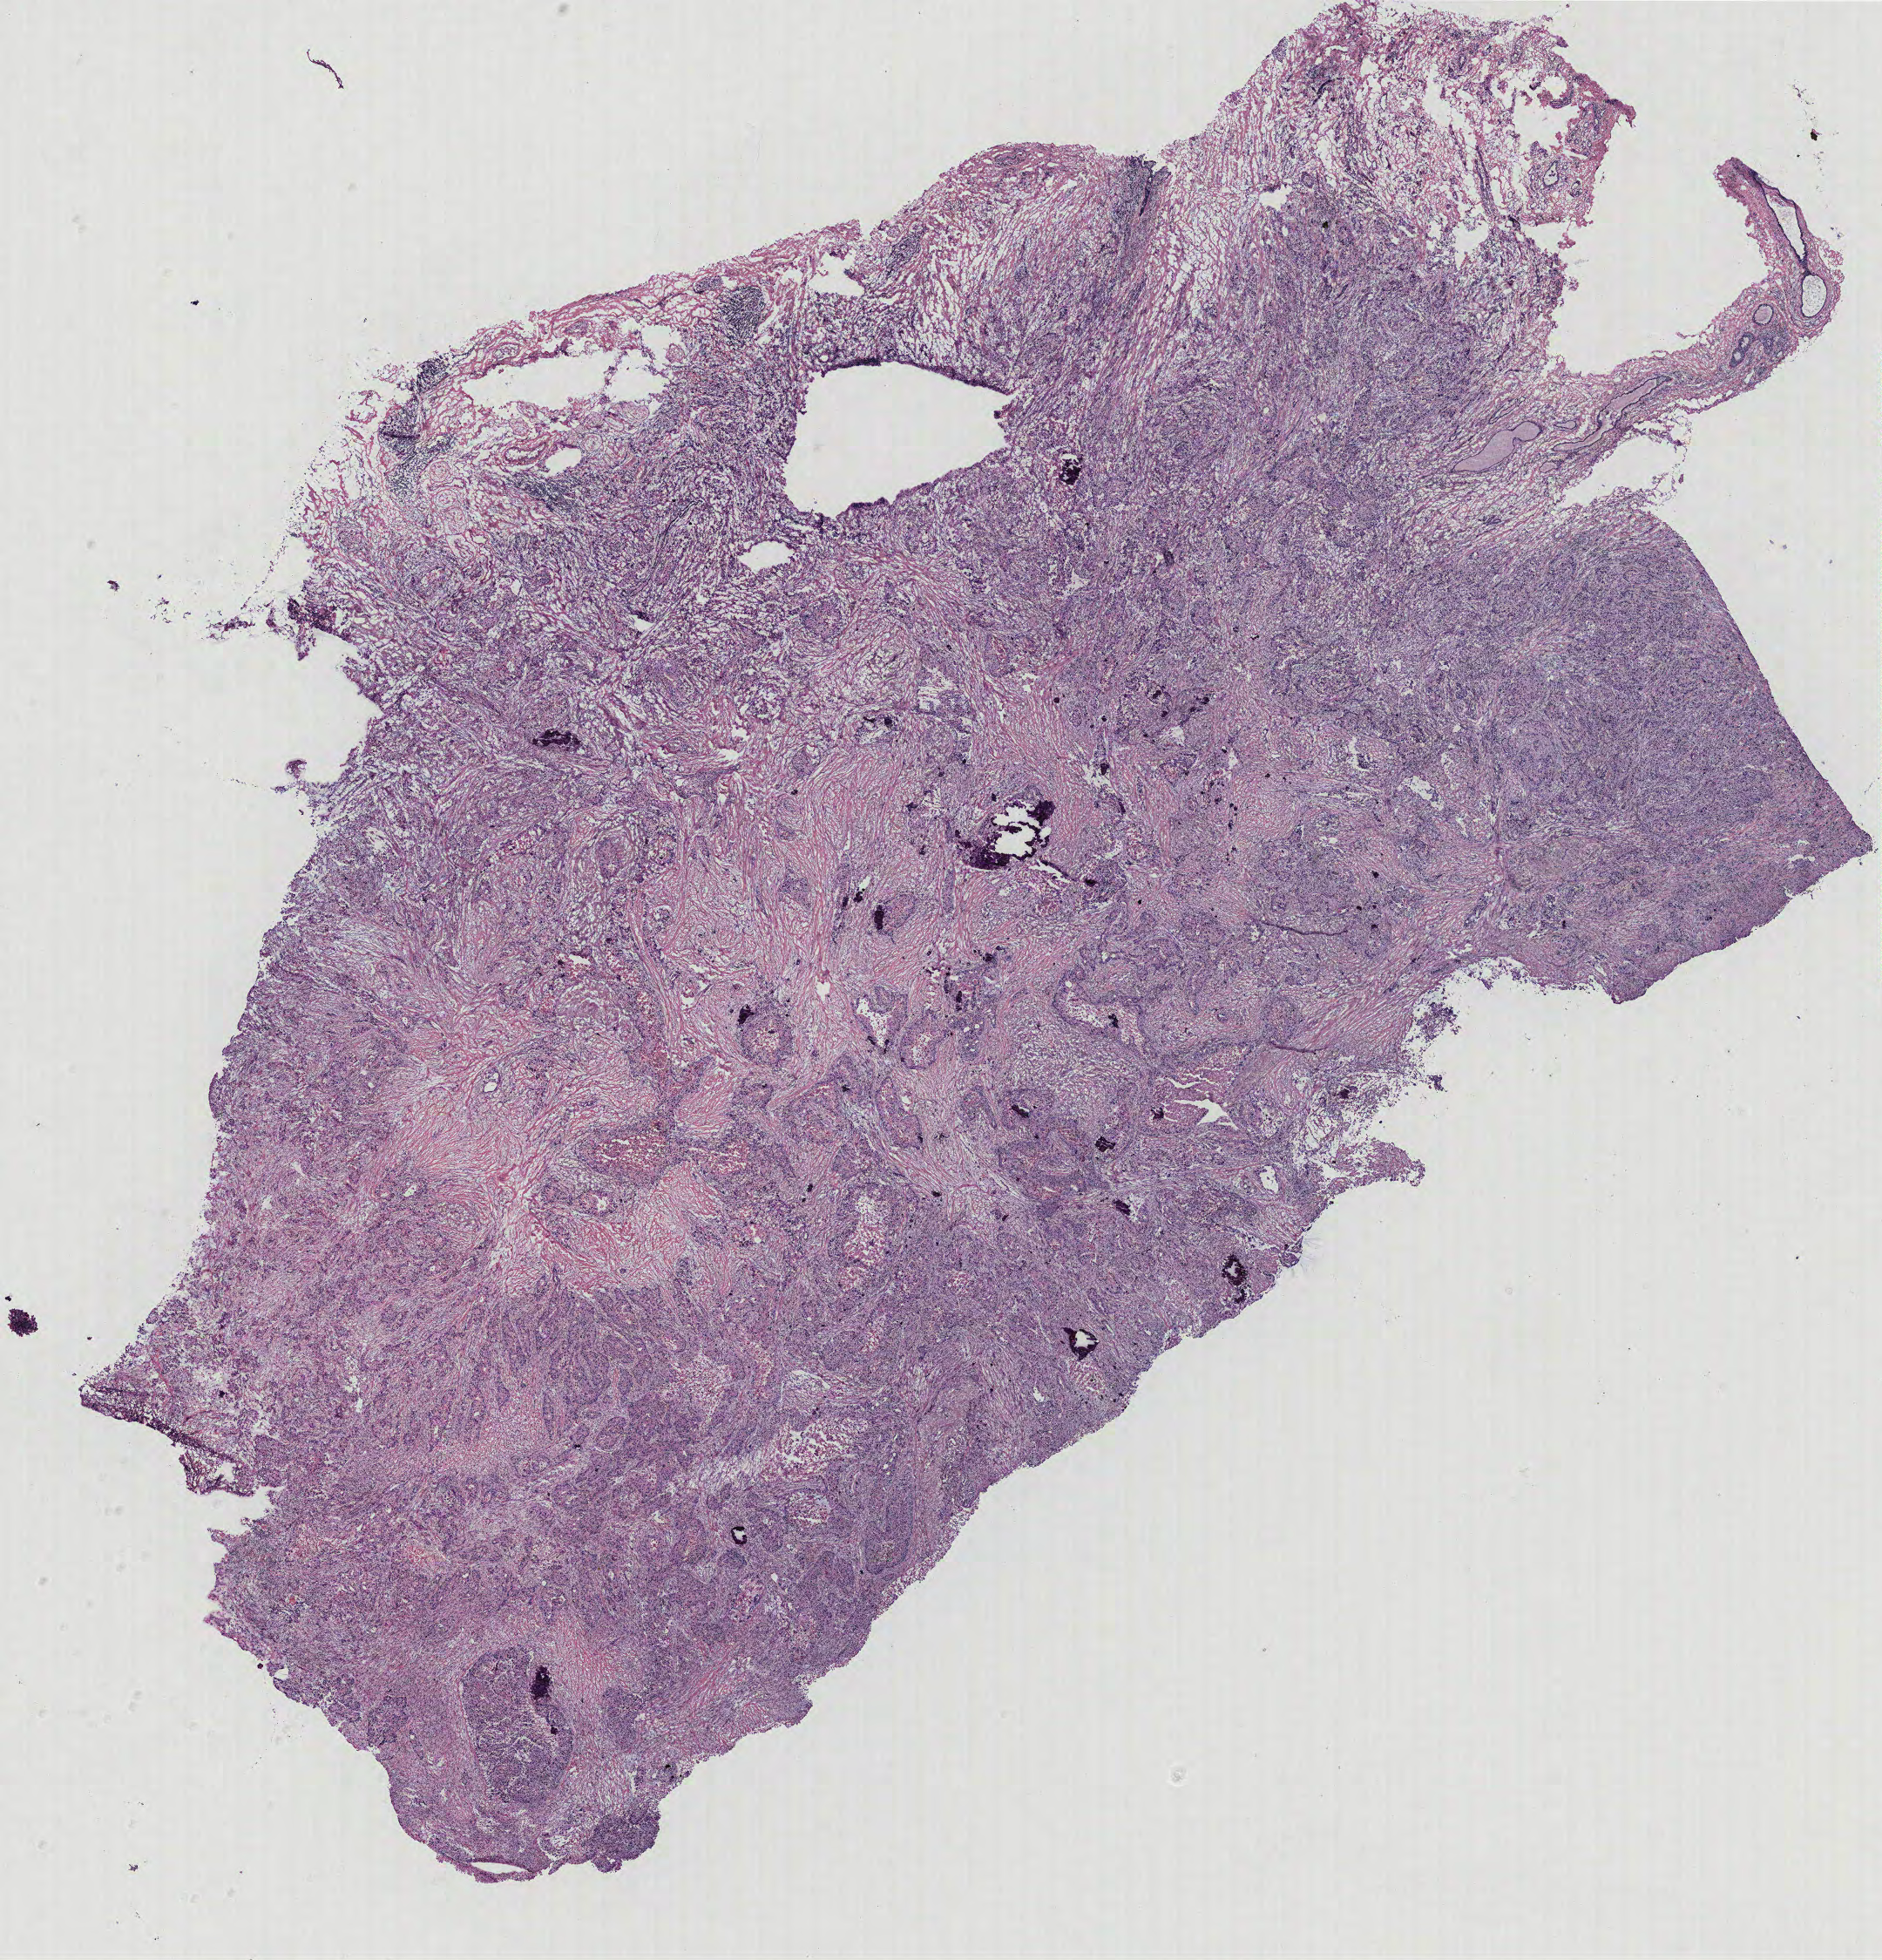
Digitized Hematoxylin and eosin (H&E) stained tissue section (whole slide) — a low-resolution overview of the entire scanned area, about 17.3 x 18.0 mm (slide scanned at 40x), breast, tissue type not recorded. 71-year-old female patient.
Patient diagnosis: Infiltrating duct carcinoma, NOS.